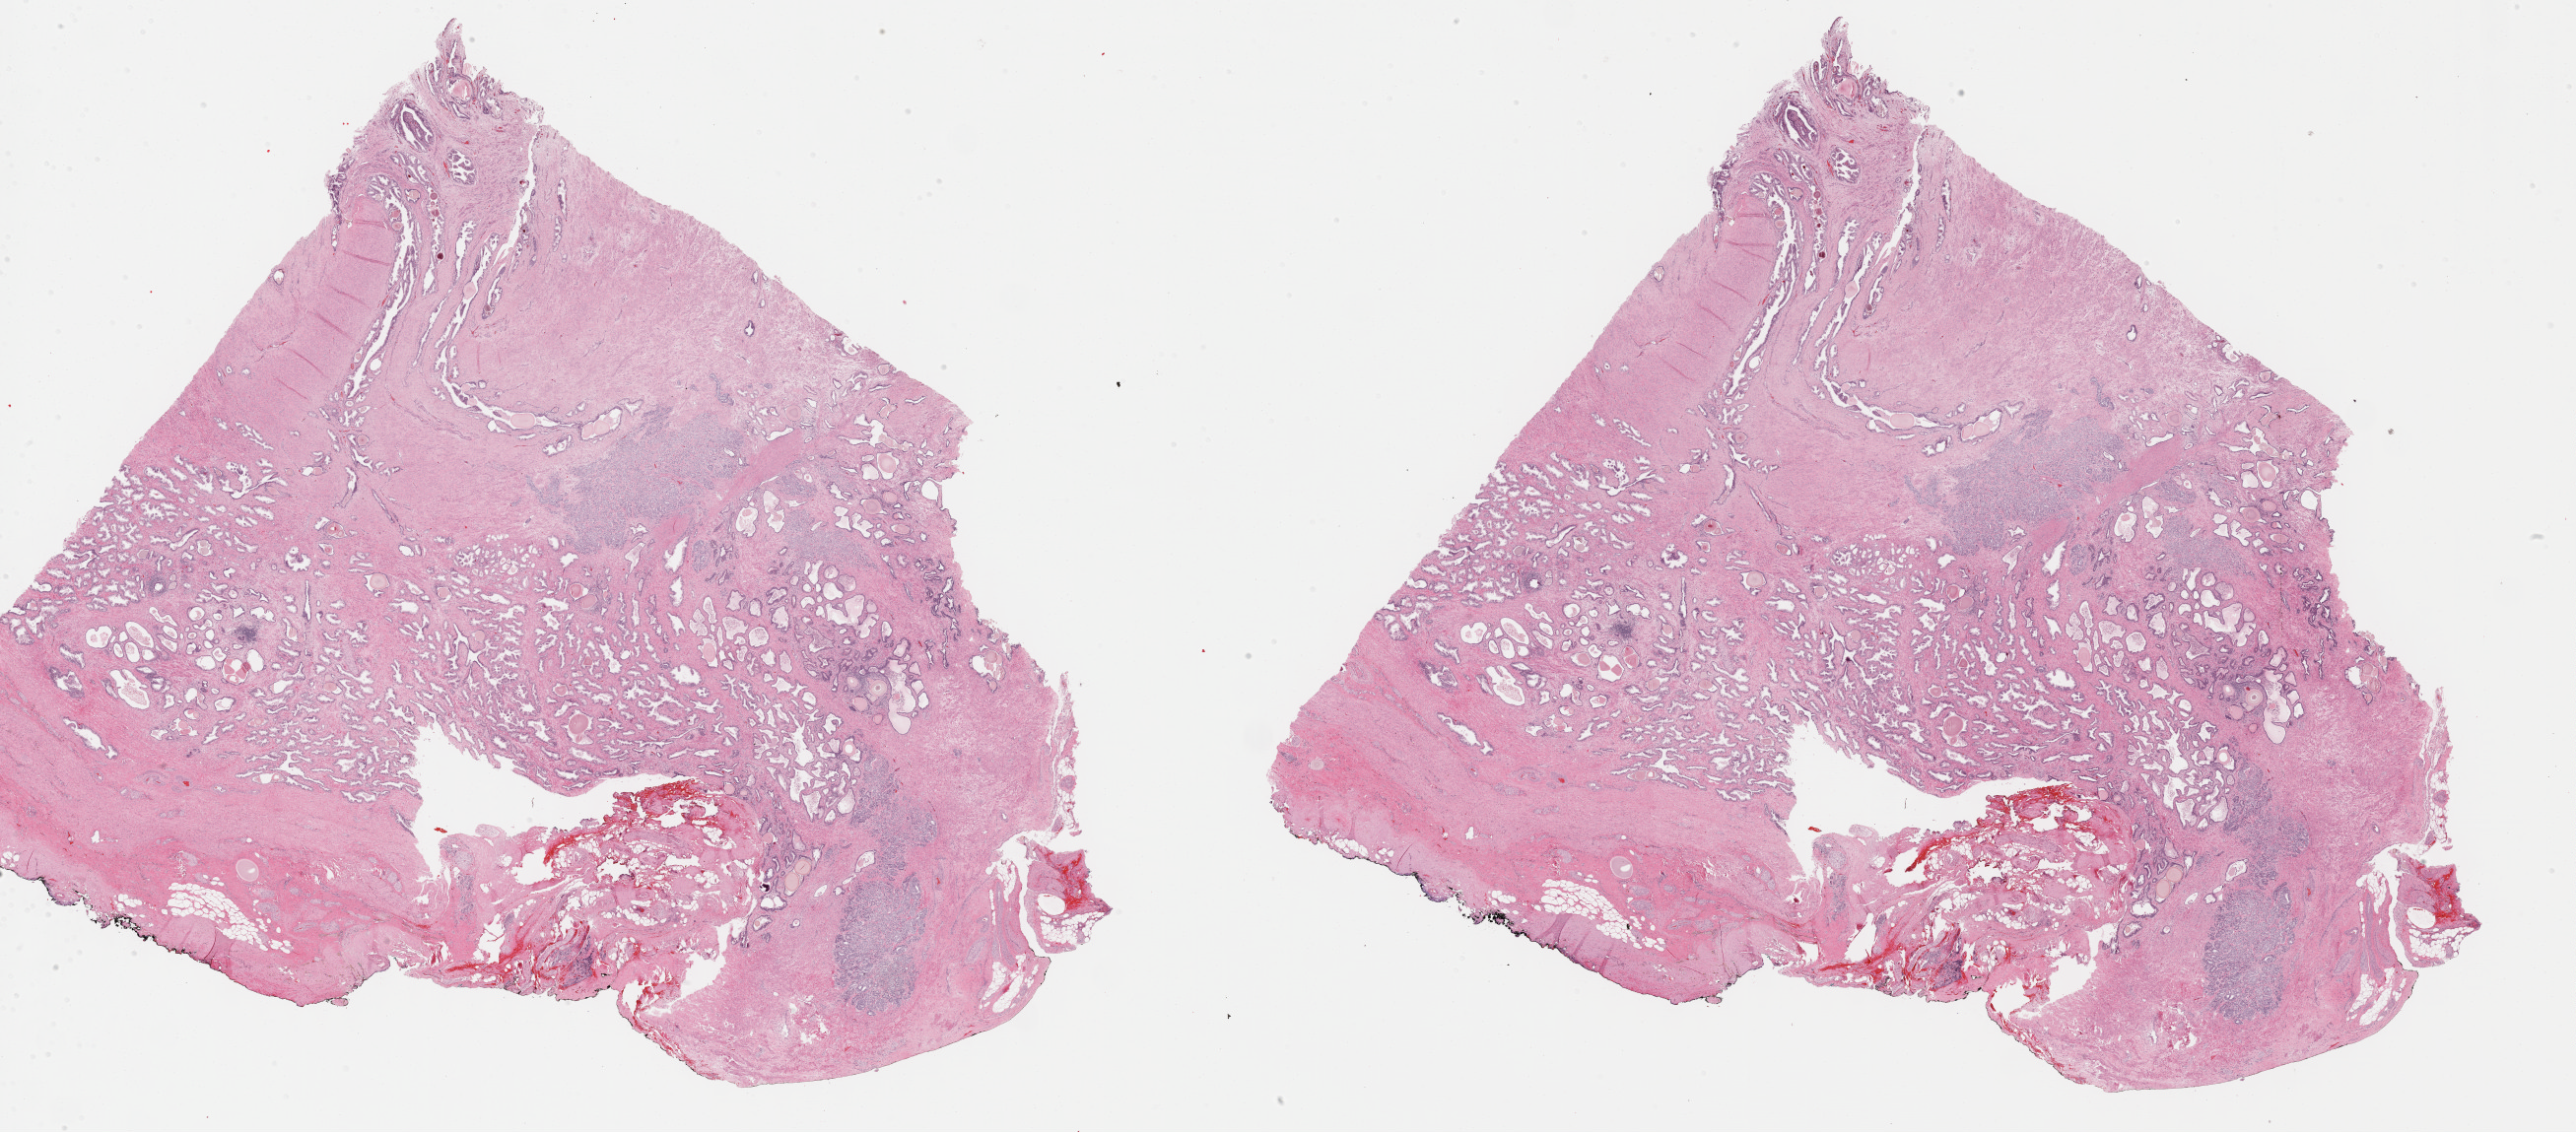
H&E-stained whole-slide image, shown as a low-resolution overview of the whole scanned area (about 42.3 x 18.6 mm). FFPE section. Primary tumour sample from the prostate. Patient: male, age at initial diagnosis 65 years. Gleason score: 9 (4+5).
Diagnosis: Adenocarcinoma, NOS (prostate gland).